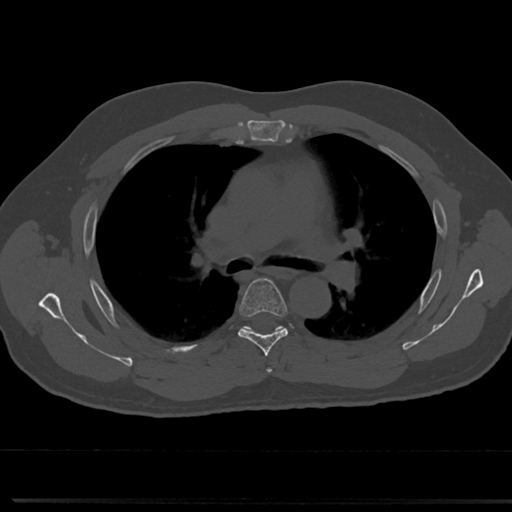
CT including the spine, one axial slice. Slice 493 of 817 in the series (ordered by position). Reconstruction kernel Br40s/3. 120 kVp. Bone window (W 1800 / L 400 HU). 0.5 mm slice thickness. 512 × 512 image matrix. Patient: male, 61 years. From the clinical record (not read from this slice): primary cancer: prostate.
Structures marked on this image (semi-automatically segmented with operator editing):
- T4 vertebra: box from (x=264, y=360) to (x=273, y=374) px
- T5 vertebra: (x=219, y=278)–(x=303, y=348)